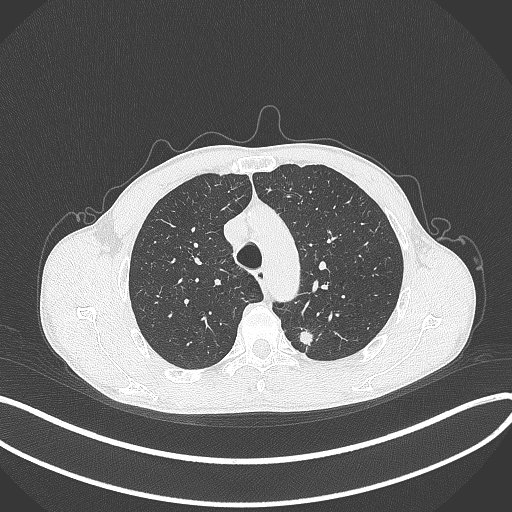
Chest CT, one axial slice. Position 301 of 429 along the scan axis. 120 kVp. Lung window (W 1500 / L -600 HU). 512 × 512 image matrix, field of view 400 × 400 mm. Patient: male, 51 years. Case-level facts recorded for this patient, not image findings: clinical TNM (as recorded): T2a N1 M1.
Structures marked on this image (rectangle marked by the reading radiologist):
- lung tumour (recorded histology: adenocarcinoma): bounding box <294,325,318,355> (left, top, right, bottom; pixels)